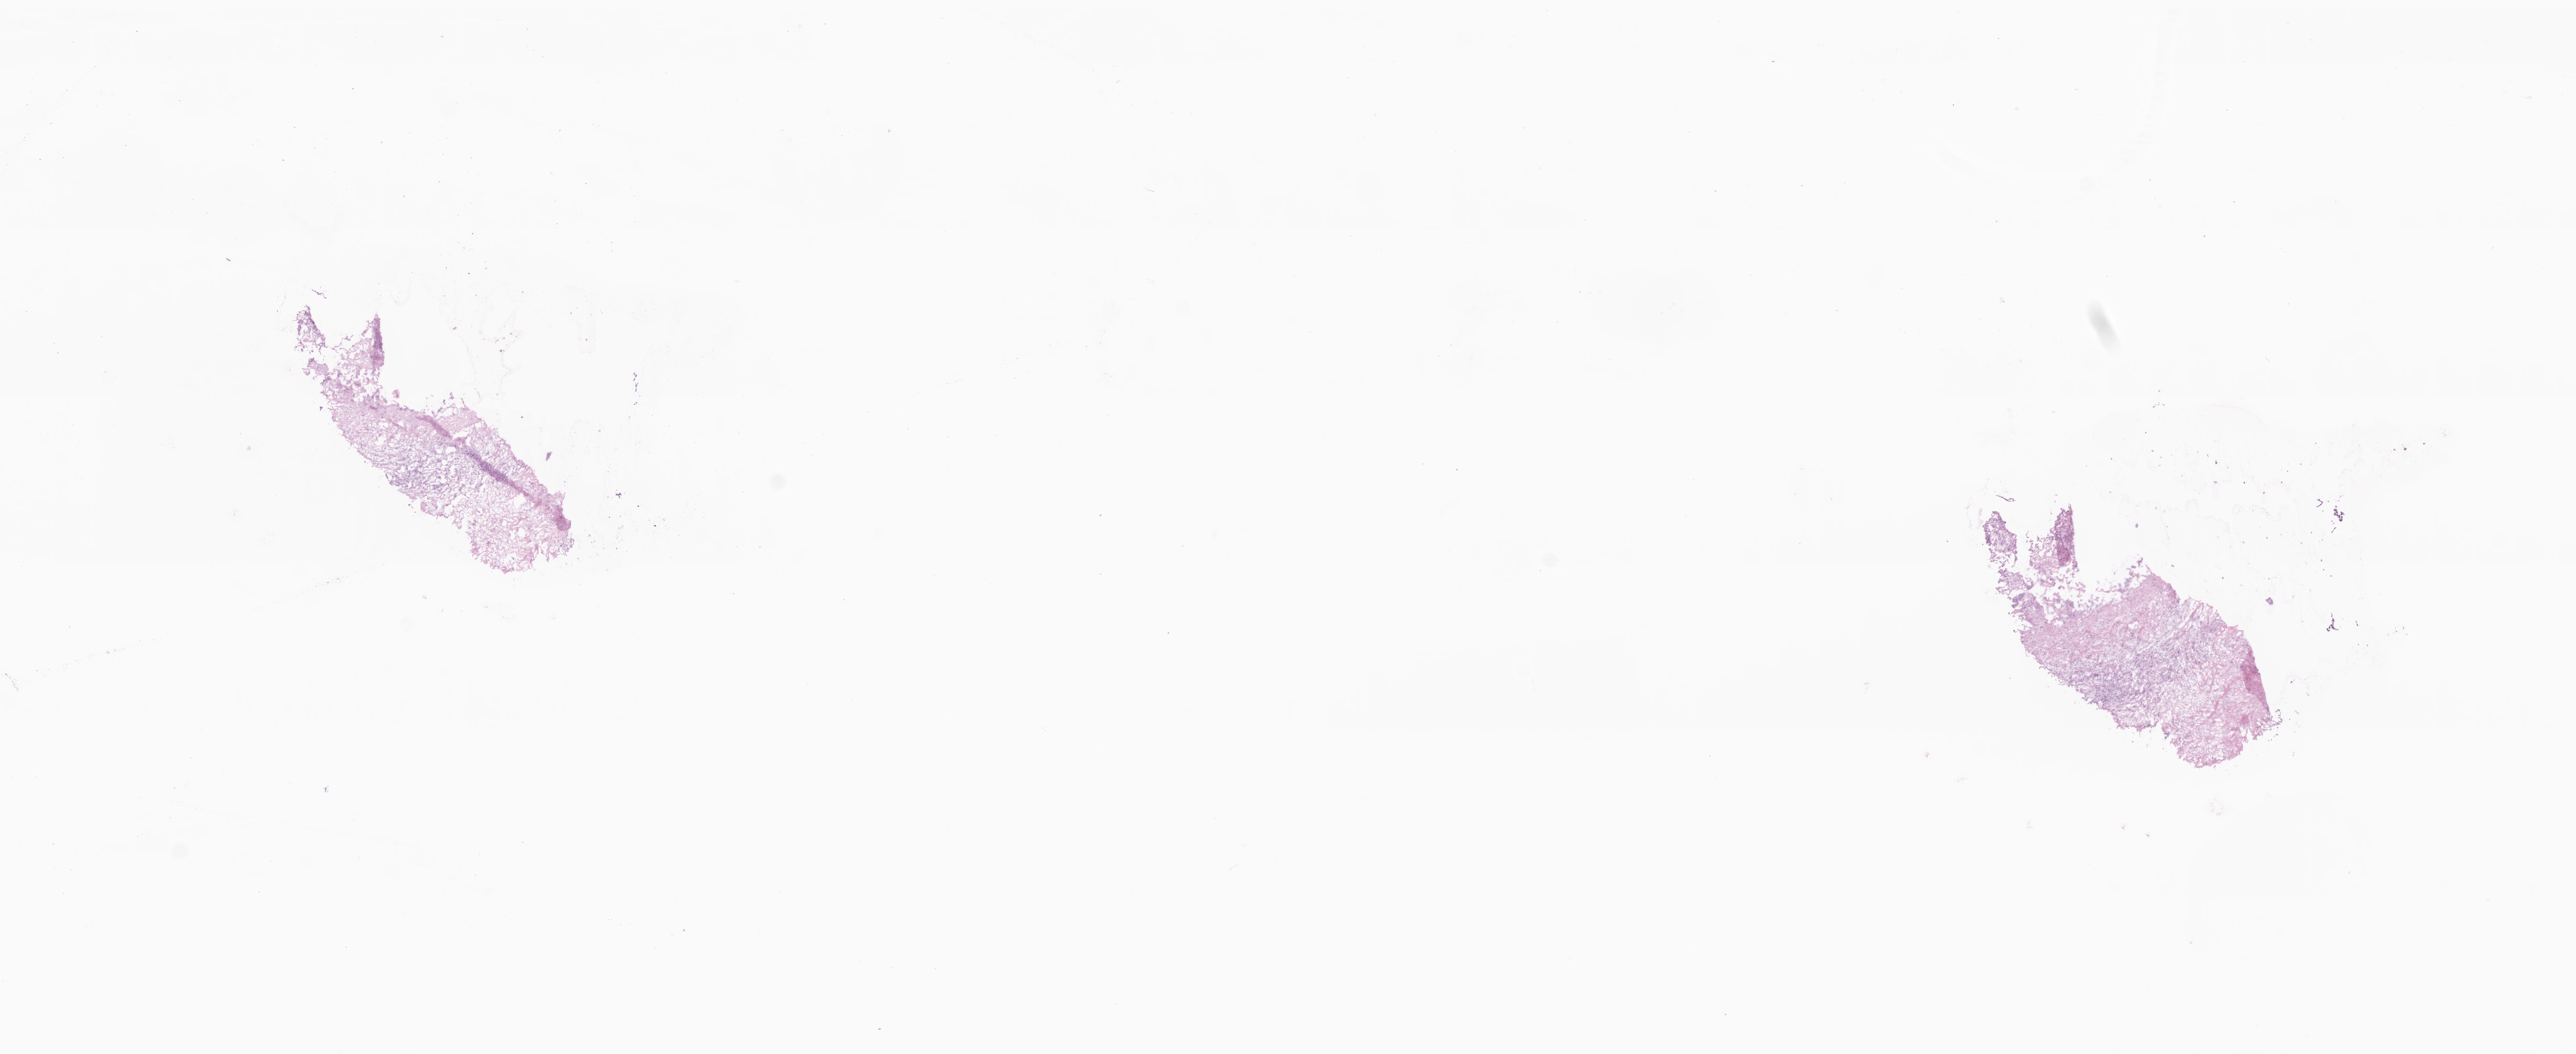
Haematoxylin and eosin whole-slide image — a low-resolution overview of the entire scanned area, about 16.5 x 6.8 mm; cryosection; metastatic tumor tissue, resected from liver. Female, age 58 years at initial diagnosis. Pathologist review of this section (percent, as recorded): tumor cells 28%, tumor nuclei 85%, stromal cells 70%, necrosis 2%, normal cells 0%. Inflammatory infiltration, as recorded: lymphocyte infiltration 5%, monocyte infiltration 0%, neutrophil infiltration 0%.
- section: top of the tissue portion
- patient diagnosis (primary): Adenocarcinoma, NOS